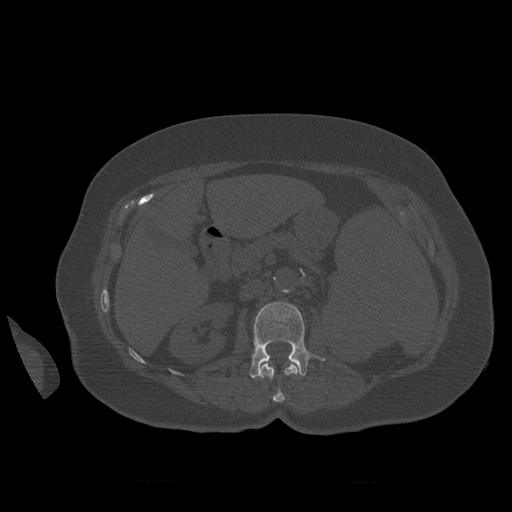
CT including the spine, one axial slice; position 261 of 399 along the scan axis; reconstruction kernel STANDARD; 120 kVp; bone window (W 1800 / L 400 HU); 512 × 512 image matrix. Patient age 81 years. Case-level facts recorded for this patient, not image findings: primary cancer: renal; vertebrae with lytic lesions (as recorded): L1.
Outlined on this slice (semi-automatic segmentation, software-assisted and operator-edited):
- L1 vertebra: bounding box (x1, y1, x2, y2) in pixels: (259, 362, 298, 403)
- L2 vertebra: (250, 302, 326, 379)